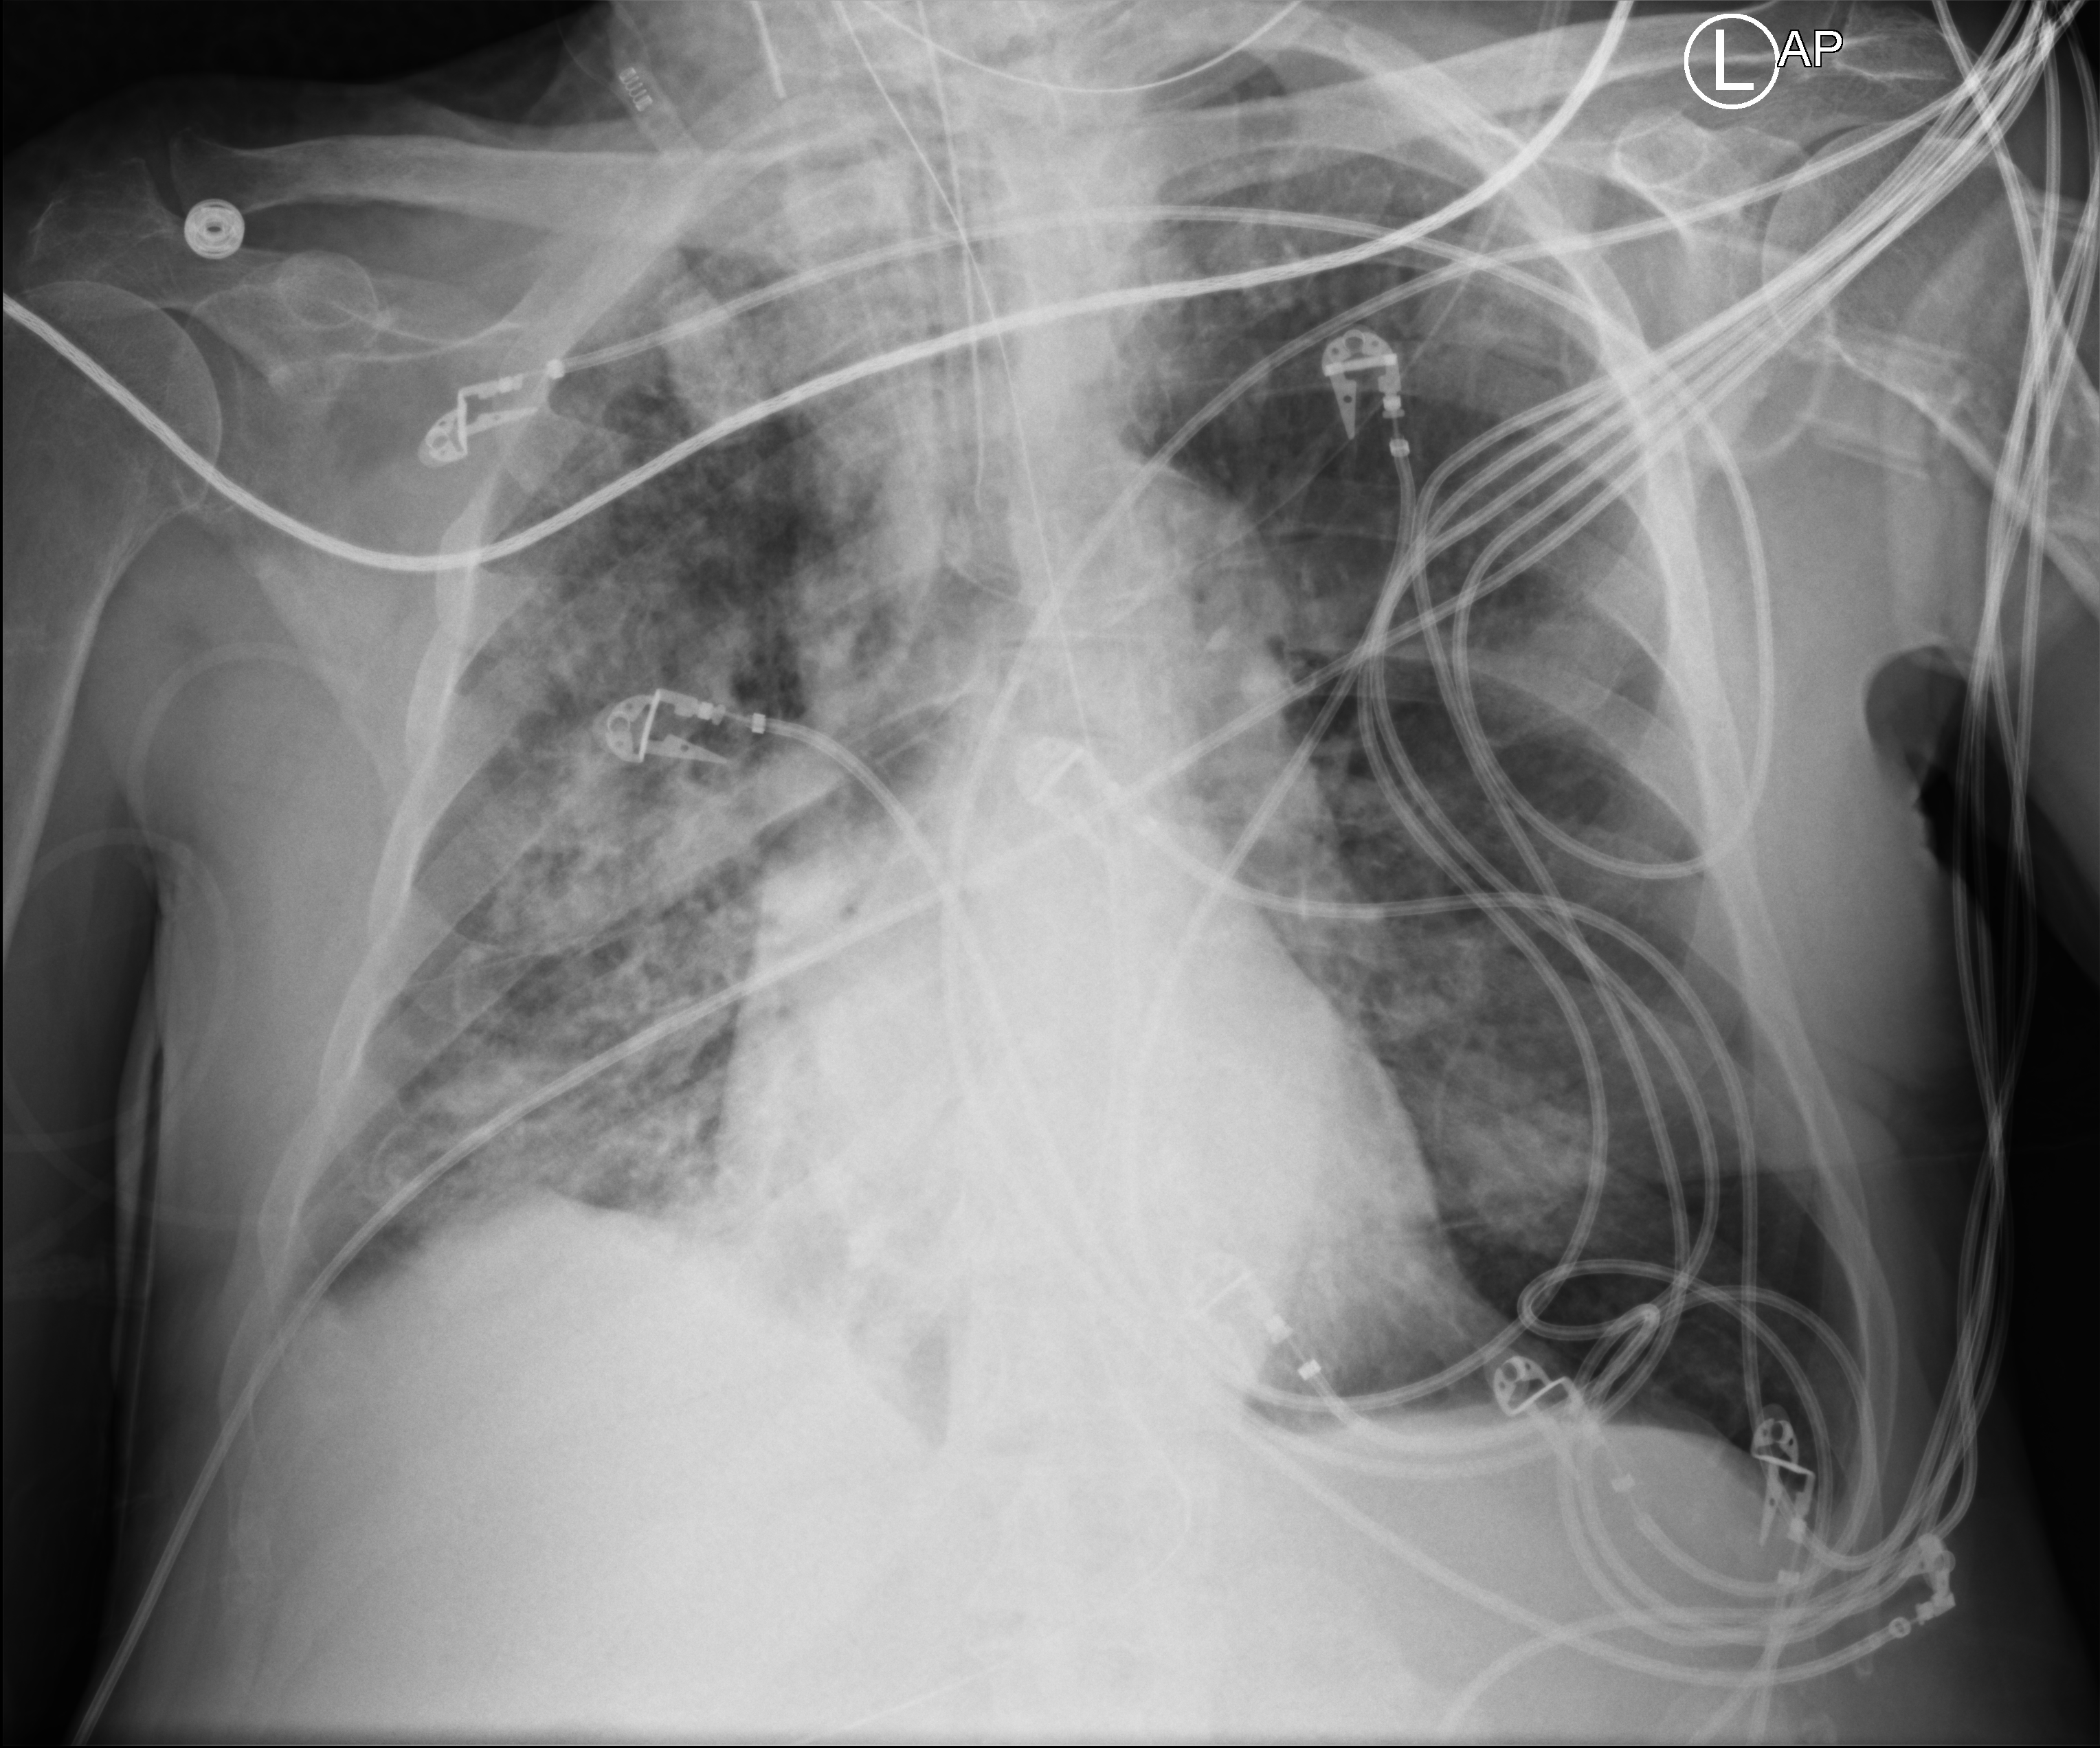
Portable chest radiograph; anteroposterior (AP) projection. Patient hospitalised with COVID-19; male, aged 75–90 years.
From the hospital-stay record, not from the radiograph (when in the stay this image was taken is not recorded): mechanically ventilated during this hospital stay: yes; other chronic lung disease (admission record): no; chronic kidney disease (admission record): no.